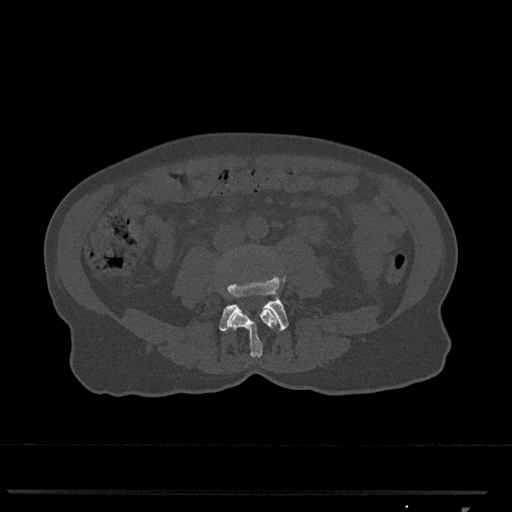
CT including the spine, one axial slice; slice 237 of 793 in the series (ordered by position); bone window (W 1800 / L 400 HU); 512 × 512 image matrix, field of view 380 × 380 mm. Patient: female, 62 years. From the clinical record (not read from this slice): primary cancer: renal.
Annotated regions visible in this slice (semi-automatic segmentation, software-assisted and operator-edited):
- L3 vertebra: box from (x=230, y=308) to (x=280, y=357) px
- L4 vertebra: (x=219, y=276)–(x=289, y=332)